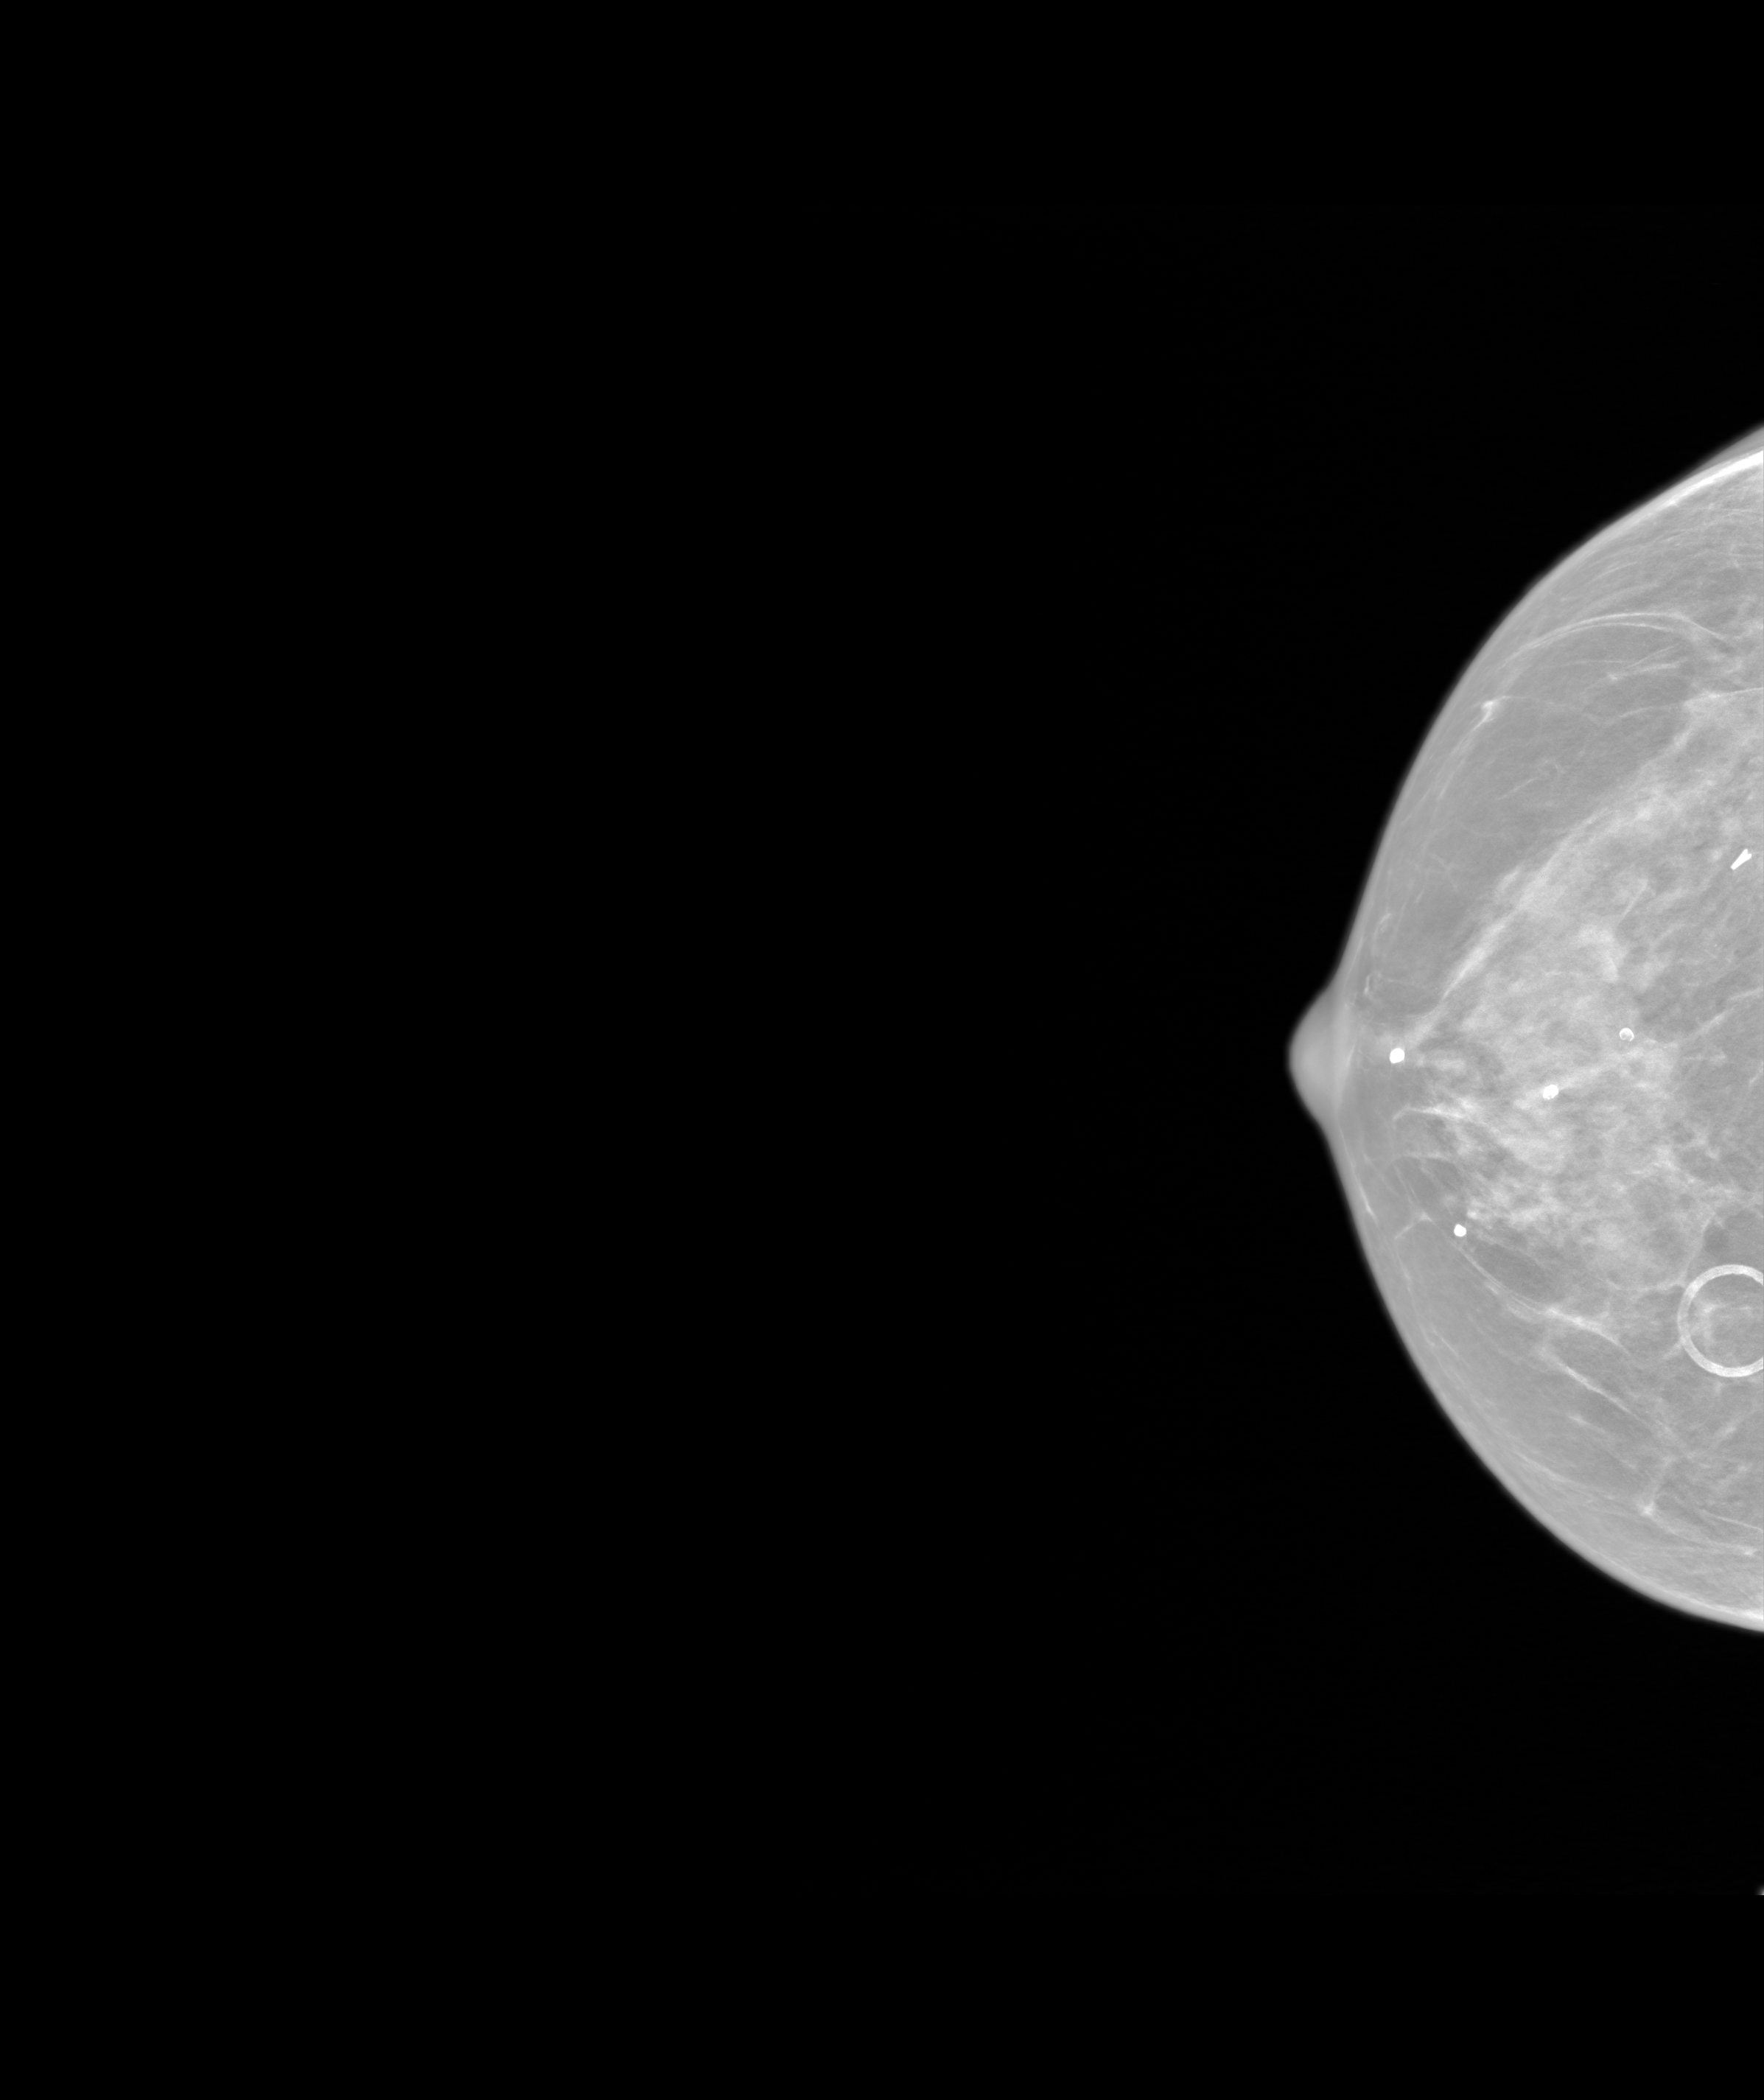
Screening examination. Patient aged 65 years (female).
Image type: synthesized 2-D view from tomosynthesis. Breast: right. Projection: craniocaudal (CC) view.